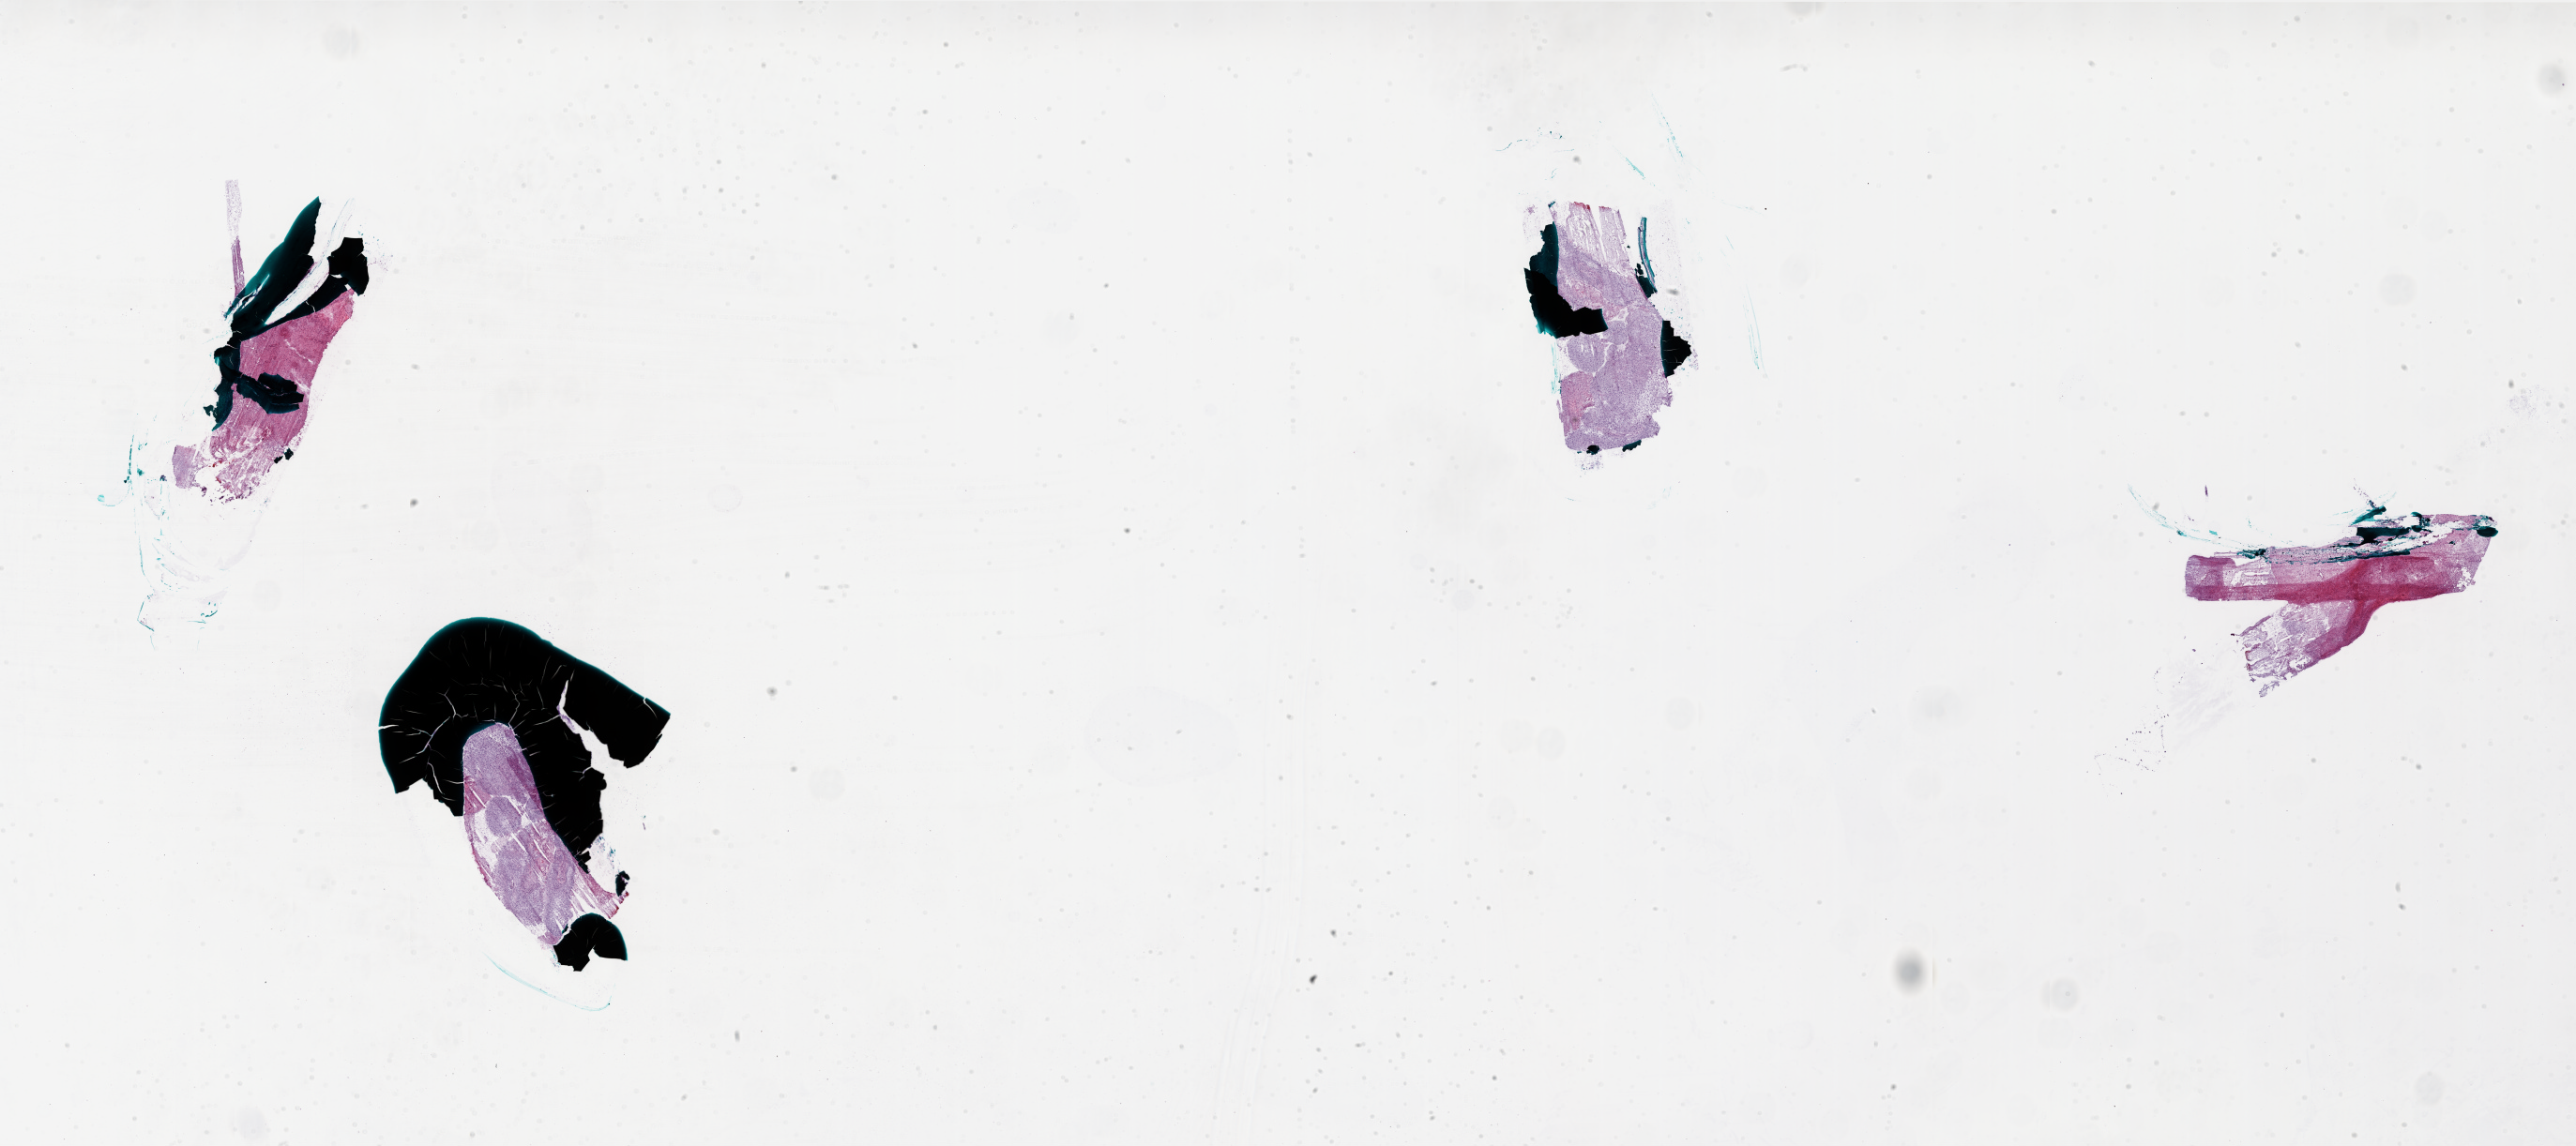
H&E whole-slide image — shown as a low-resolution overview of the whole scanned area (about 44.0 x 19.6 mm, slide scanned at 20x). Frozen section from the bottom of the tissue portion. Primary tumour sample from the brain. Patient: female, age at initial diagnosis 72 years. Composition of this section per pathologist review: tumour cells 85%, tumour nuclei 90%, normal cells 0%, stromal cells 5%, necrosis 10%.
Pathologic diagnosis: Glioblastoma.